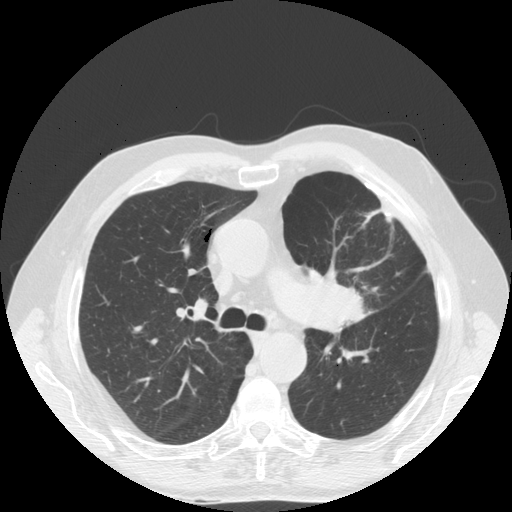
Low-dose screening chest CT, one axial slice. Slice 115 of 170 in the series (ordered by position). Reconstruction kernel STANDARD. 140 kVp. Lung window (W 1500 / L -600 HU). 2.5 mm slice thickness. 512 × 512 image matrix, field of view 380 × 380 mm.
Outlined on this slice (outlined manually by an expert reader):
- lesion 1 (tumor, upper lobe of left lung): bounding box <306,268,365,324> (left, top, right, bottom; pixels)